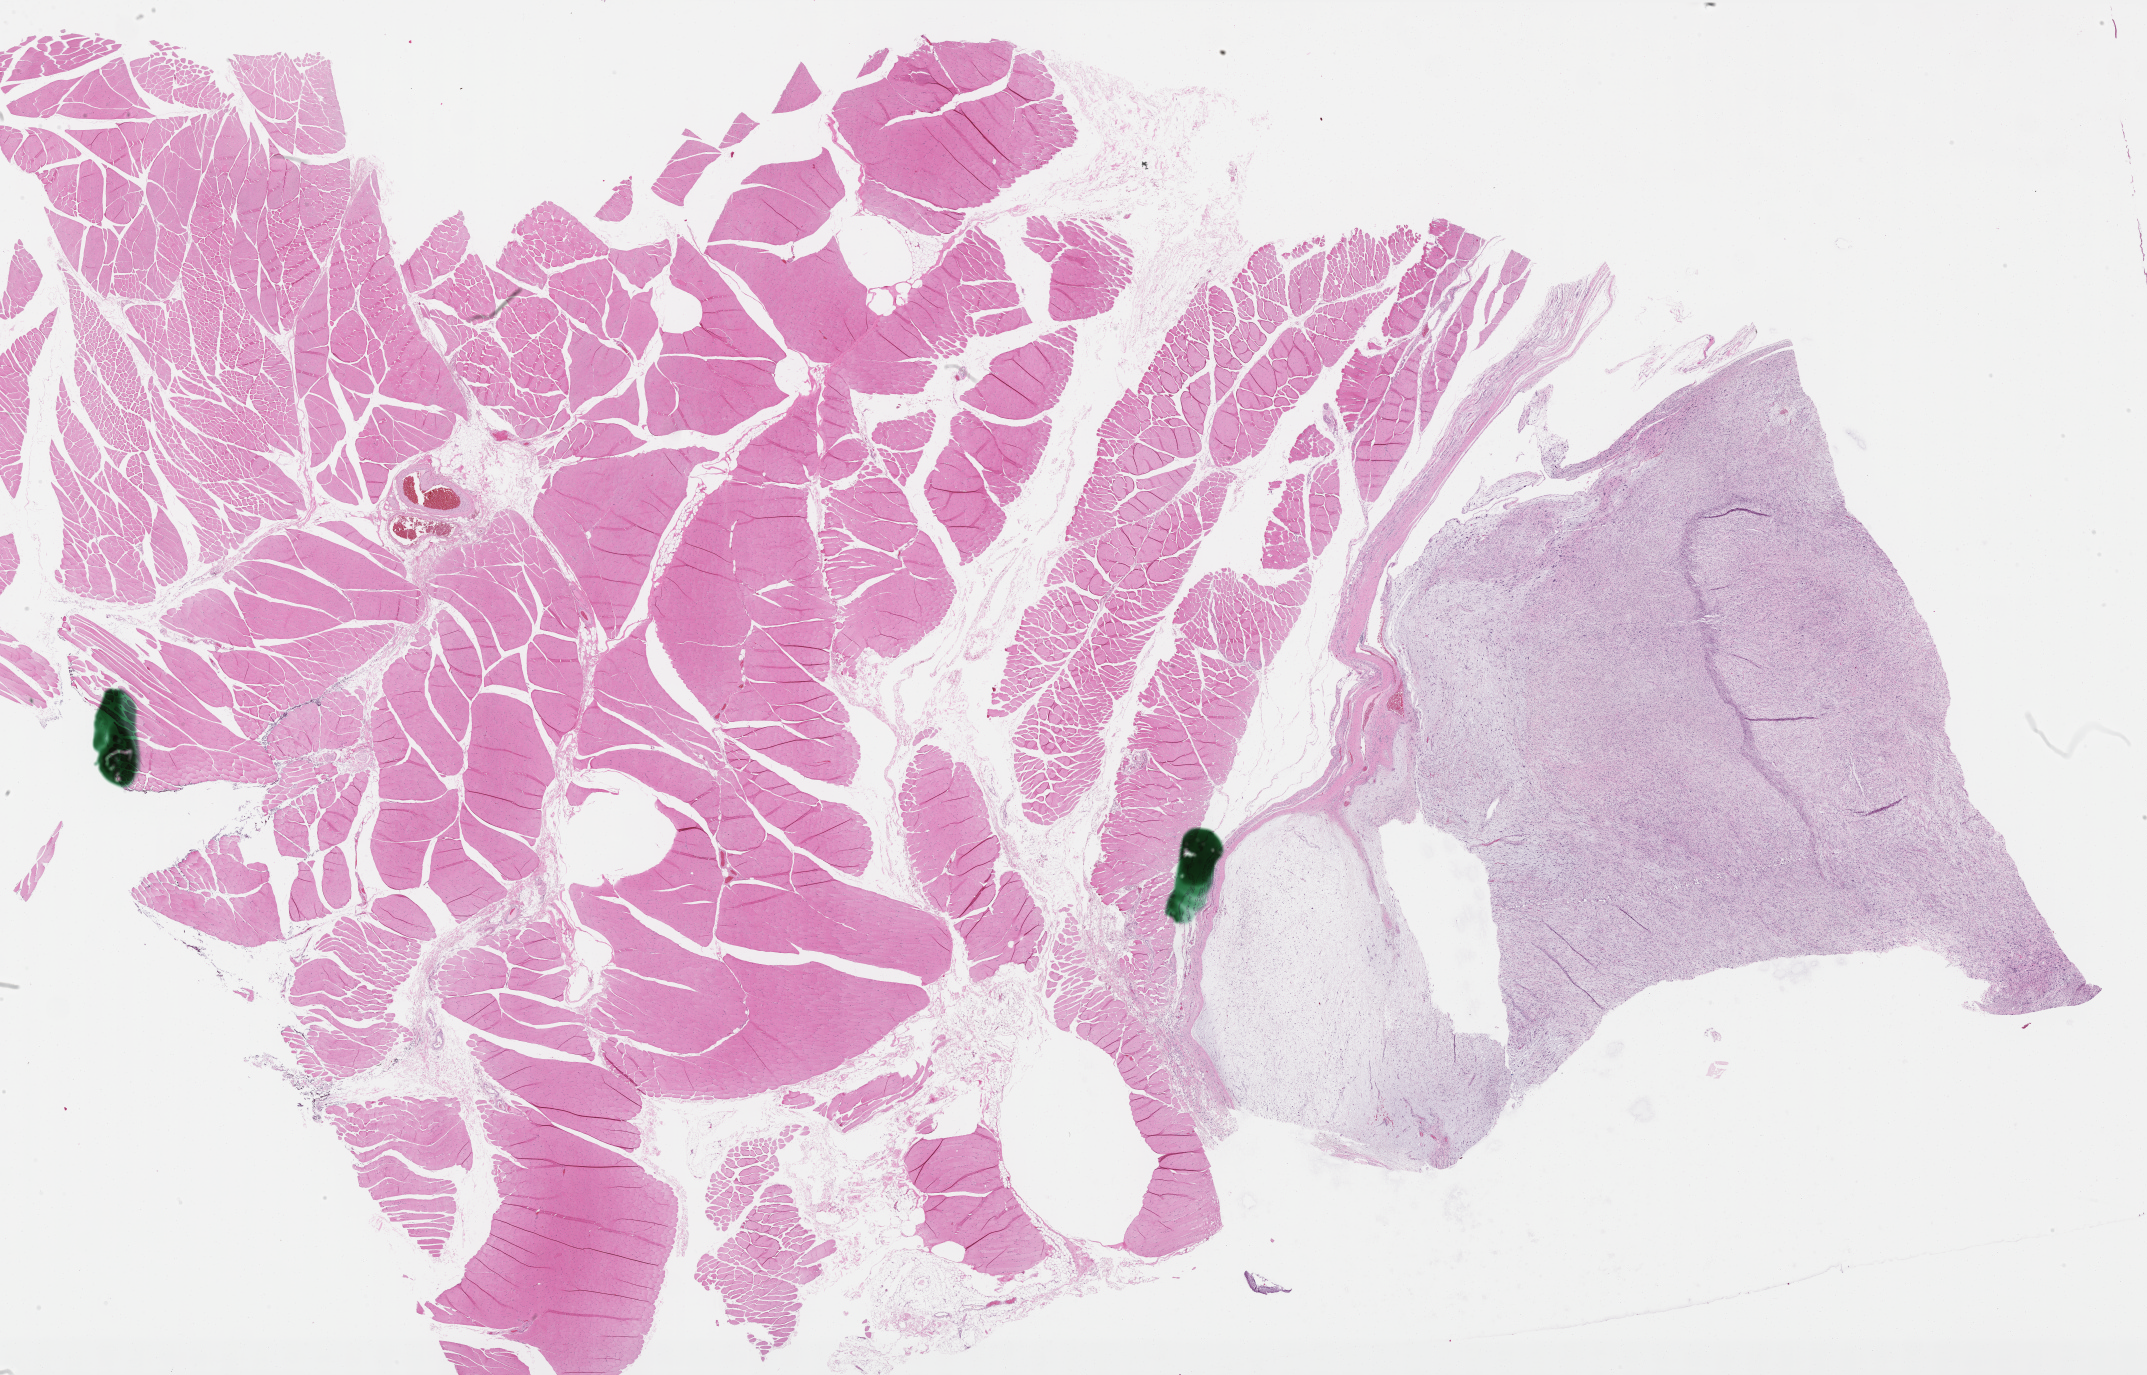
Digitized H&E tissue section (whole slide), a low-resolution overview of the entire scanned area, about 34.5 x 22.1 mm, formalin-fixed paraffin-embedded (FFPE) diagnostic section, sample: primary tumour, connective, subcutaneous and other soft tissues. Male, age 75 years at initial diagnosis.
Histologic diagnosis: Fibromyxosarcoma.